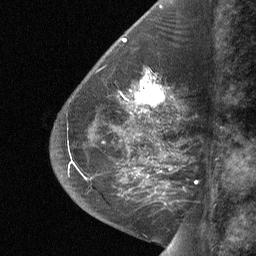
Breast MRI (dynamic contrast-enhanced), one sagittal slice; position 26 of 64 along the scan axis; dynamic contrast-enhanced study with each time point stored as its own series, time point 2 of 3 at this slice position (early post-contrast, ordered by acquisition time); 1.5 T; TE 4.8 ms, TR 27 ms; 2 mm slice thickness; 256 × 256 image matrix, field of view 180 × 180 mm. Female patient, age 59 years. Case-level facts recorded for this patient, not image findings: setting: breast cancer imaged before/during neoadjuvant chemotherapy; receptor status: triple-negative.
Structures marked on this image (semi-automatically segmented with operator editing):
- analysis volume of interest (the breast-tissue region the enhancement analysis was run in; not a lesion): bounding box (x1, y1, x2, y2) in pixels: (126, 75, 173, 114)
- tumour enhancement mask (voxels above the 90 % enhancement threshold inside the analysis volume of interest): (130, 76, 172, 110)